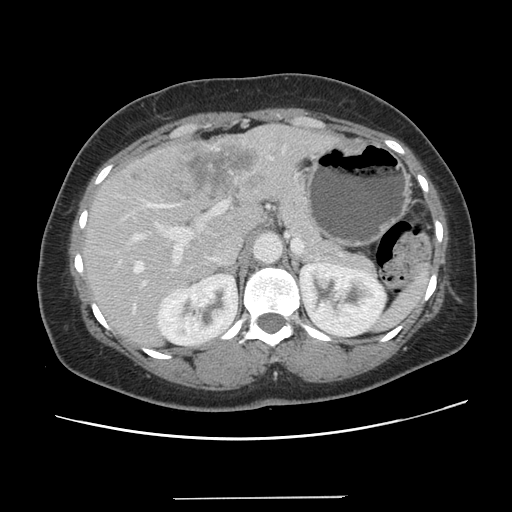
Contrast-enhanced abdominal CT, one axial slice; position 82 of 141 along the scan axis; 120 kVp; intravenous contrast given; soft-tissue window (W 400 / L 40 HU); 2.5 mm slice thickness; 512 × 512 image matrix. Female patient, age 53 years. Case-level facts recorded for this patient, not image findings: diagnosis: colorectal cancer liver metastases, imaged before liver resection.
Annotated regions visible in this slice (expert manual segmentation):
- hepatic veins: box from (x=133, y=203) to (x=170, y=310) px
- liver: (x=83, y=126)–(x=336, y=345)
- planned liver remnant (the part of the liver to remain after resection): (x=84, y=206)–(x=262, y=346)
- portal vein (with intrahepatic branches): (x=132, y=202)–(x=225, y=289)
- liver metastasis: (x=133, y=141)–(x=264, y=203)